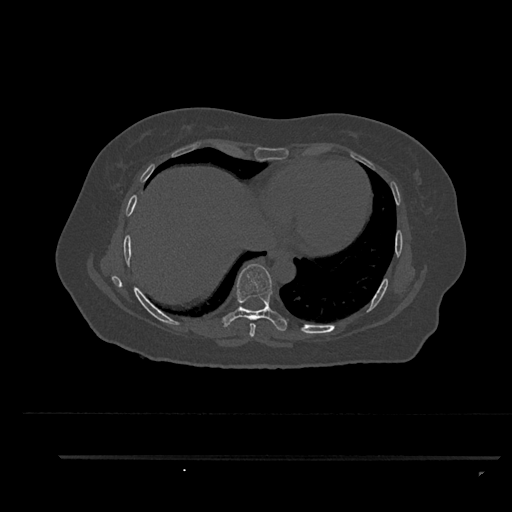
CT including the spine, one axial slice. Position 466 of 797 along the scan axis. Reconstruction kernel Br40s/3. 120 kVp. Bone window (W 1800 / L 400 HU). 0.5 mm slice thickness. 512 × 512 image matrix. Female patient, age 44 years. Case-level facts recorded for this patient, not image findings: primary cancer: renal; vertebrae with lytic lesions (as recorded): L1.
Annotated regions visible in this slice (semi-automatically segmented with operator editing):
- T7 vertebra: bounding box (x1, y1, x2, y2) in pixels: (249, 323, 256, 337)
- T8 vertebra: (222, 264, 287, 331)